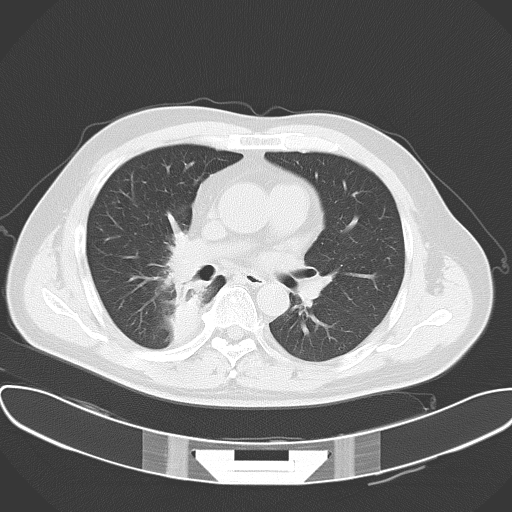
Chest CT, one axial slice; slice 31 of 57 in the series (ordered by position); reconstruction kernel B70f; 120 kVp; lung window (W 1500 / L -600 HU); 5 mm slice thickness; 512 × 512 image matrix, field of view 388 × 388 mm. Patient: male, 48 years. Case-level facts recorded for this patient, not image findings: clinical TNM (as recorded): T1a N1 M1c; histopathological grade: G3.
Structures marked on this image (rectangle marked by the reading radiologist):
- lung tumour (recorded histology: adenocarcinoma): box from (x=158, y=229) to (x=220, y=295) px